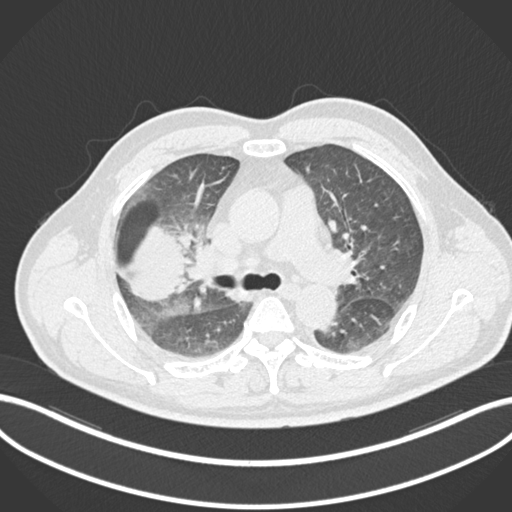
Chest CT, one axial slice. Position 648 of 852 along the scan axis. Reconstruction kernel B30f. 120 kVp. Lung window (W 1500 / L -600 HU). 1 mm slice thickness. 512 × 512 image matrix, field of view 400 × 400 mm. Male patient, age 55 years. From the clinical record (not read from this slice): clinical TNM (as recorded): T3 N2 M1.
Annotated regions visible in this slice (rectangle marked by the reading radiologist):
- lung tumour (recorded histology: adenocarcinoma): box from (x=119, y=220) to (x=188, y=302) px